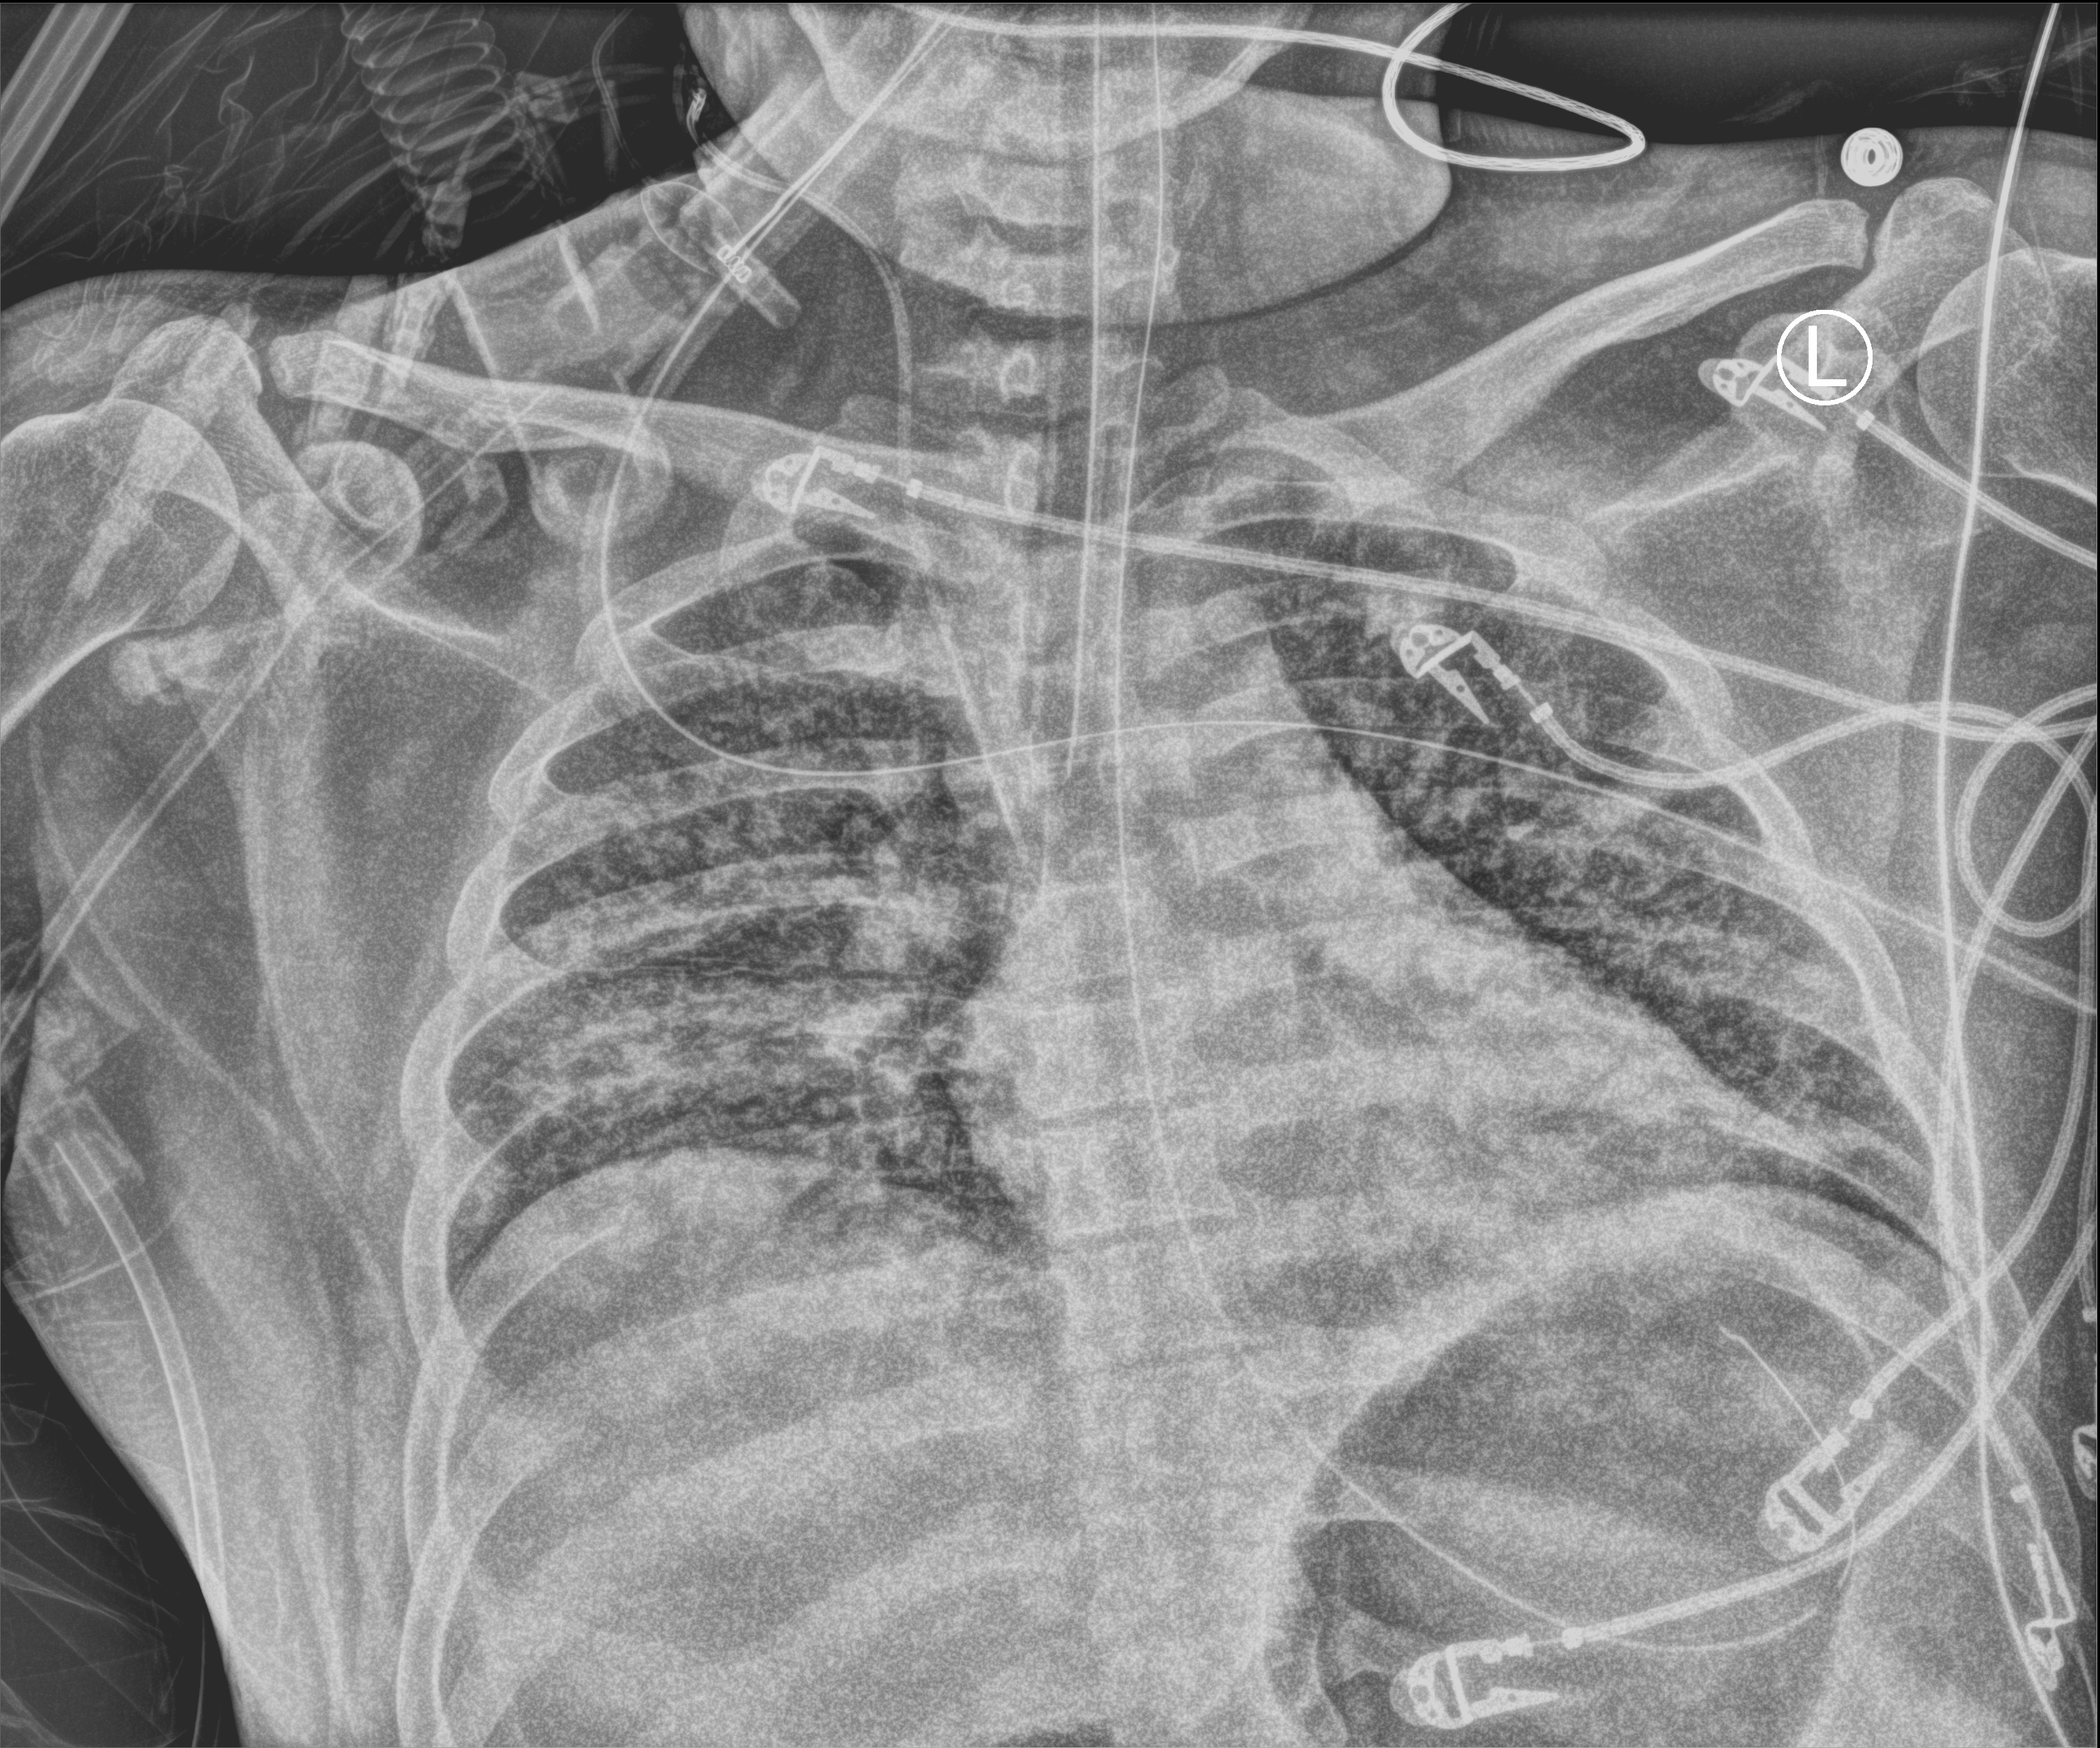
Portable chest radiograph, anteroposterior (AP) projection. Patient hospitalised with COVID-19; male, aged 18–59 years.
From the hospital-stay record, not from the radiograph (when in the stay this image was taken is not recorded):
- admitted to intensive care during this hospital stay: yes
- mechanically ventilated during this hospital stay: yes
- length of hospital stay: 44 days